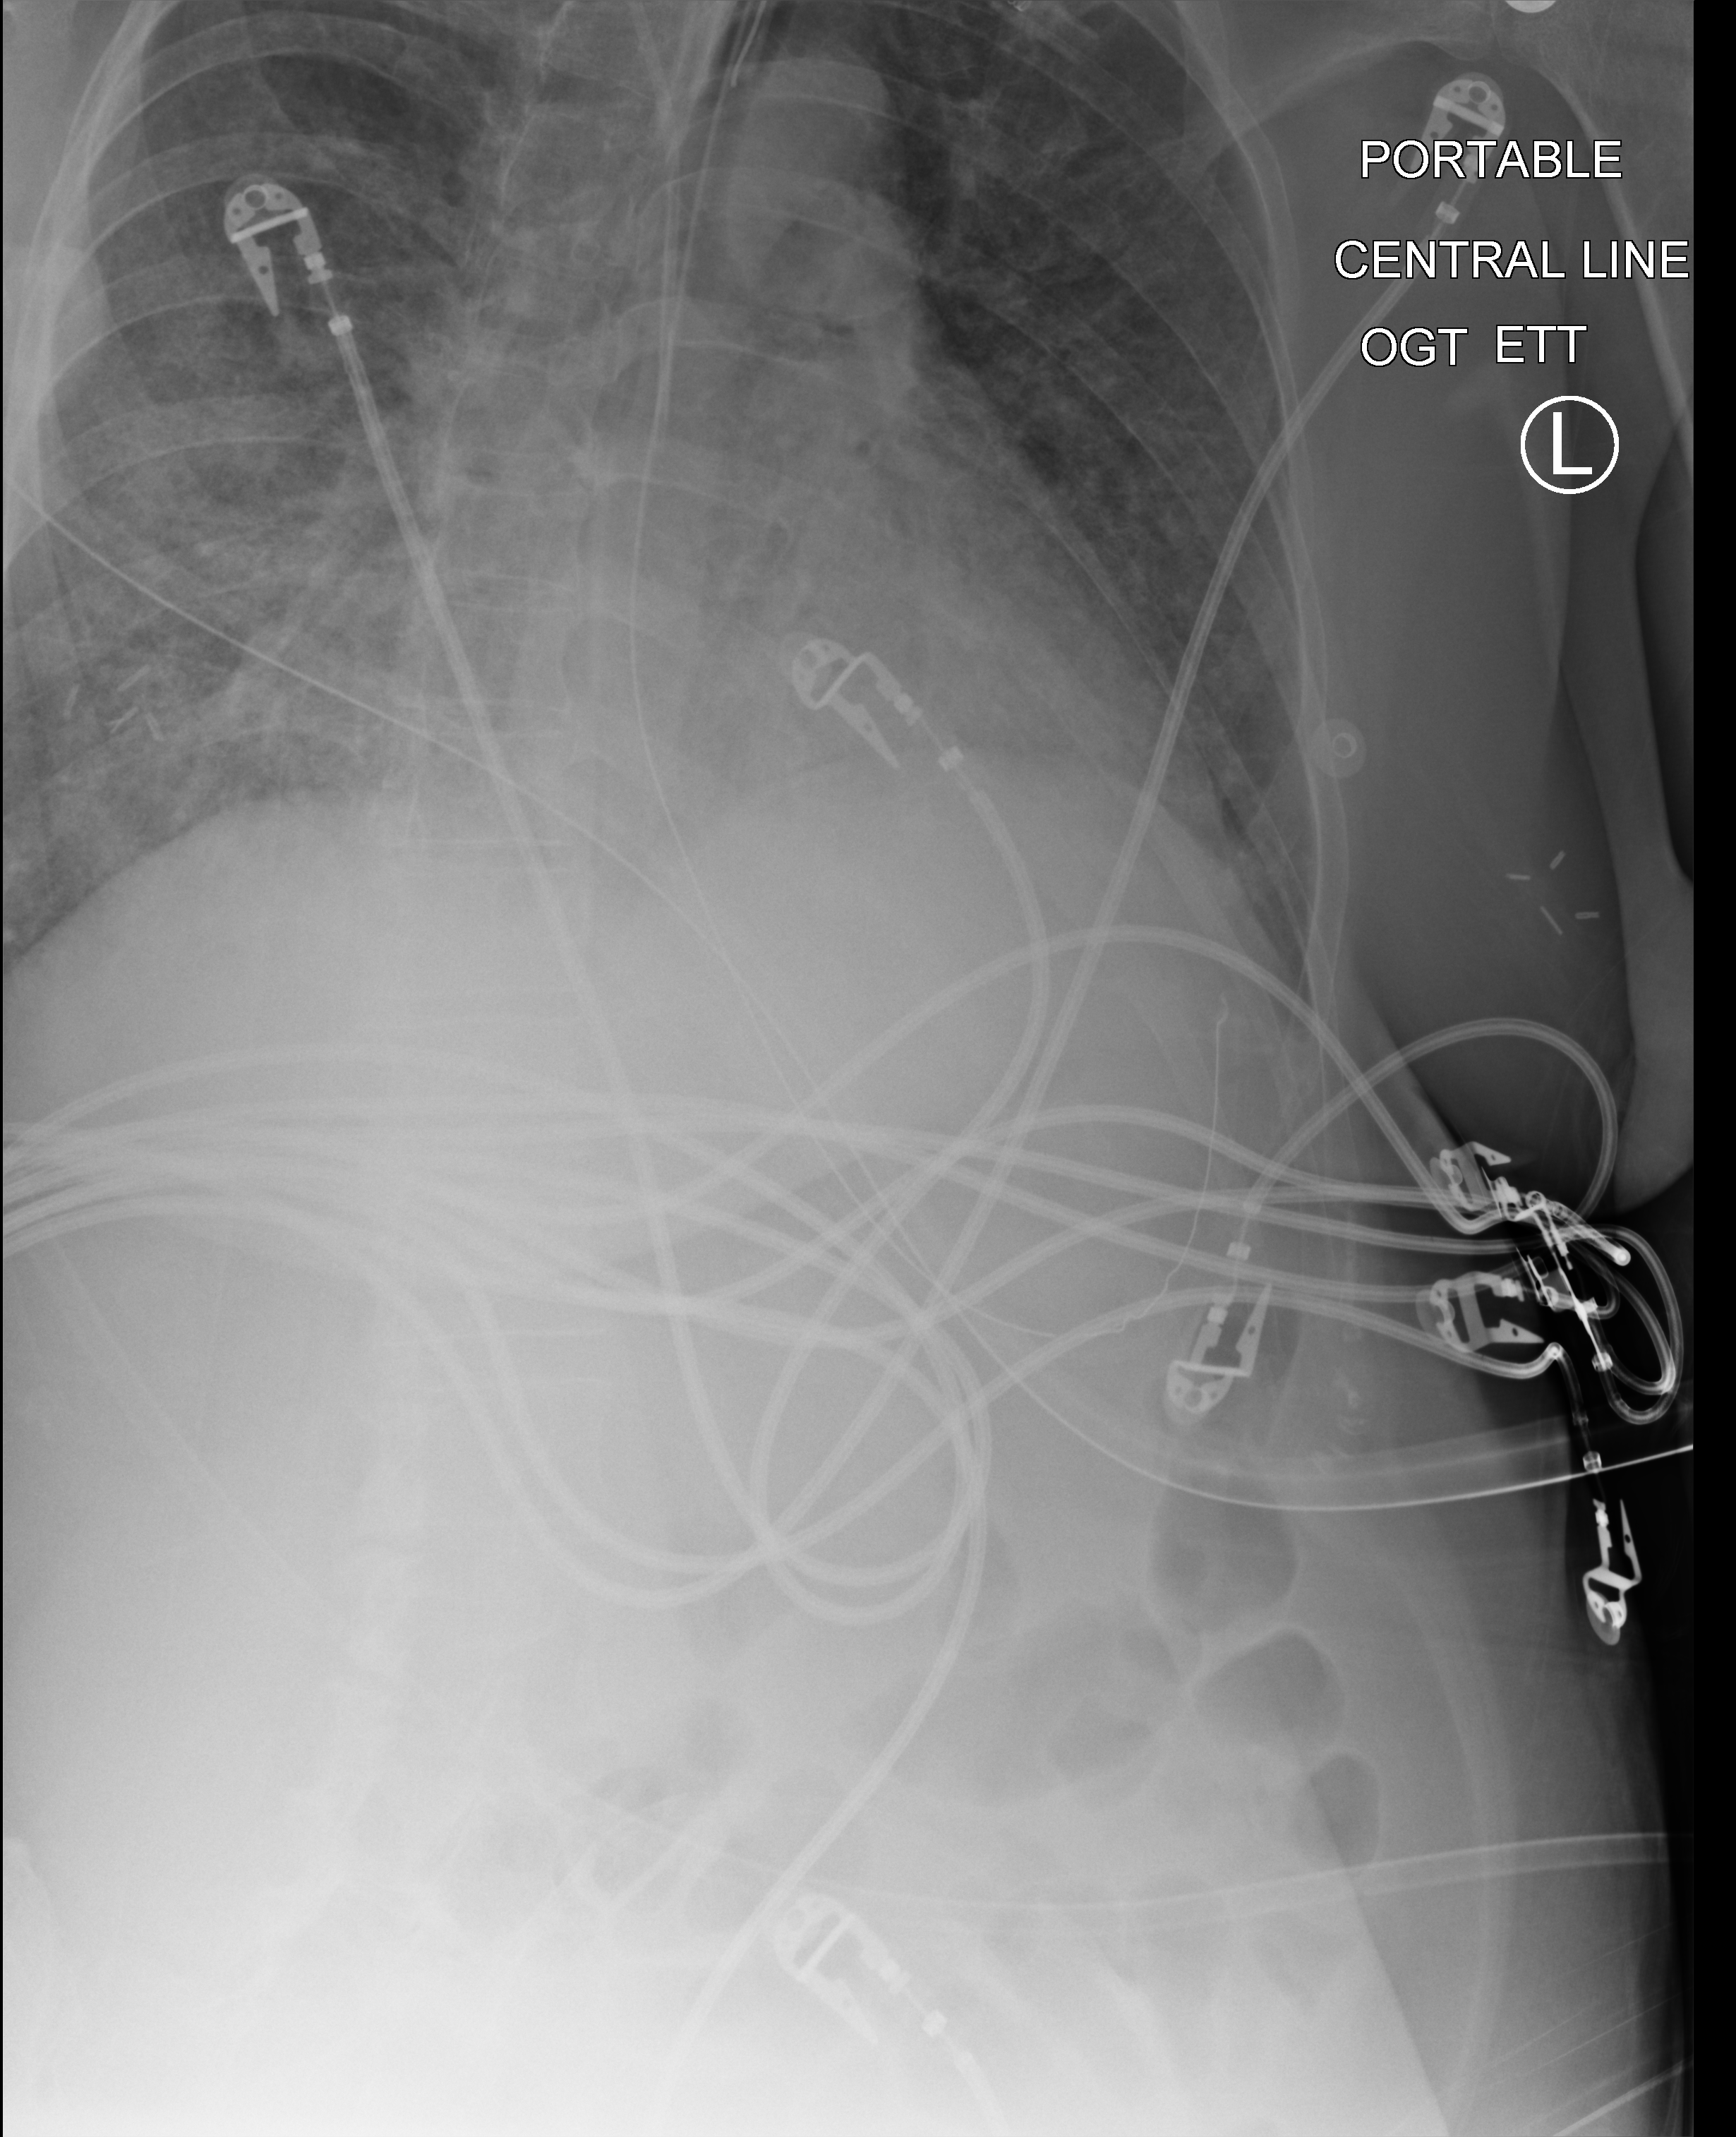
Chest X-ray (portable), anteroposterior (AP) projection. Patient hospitalised with COVID-19; female, aged 18–59 years.
From the hospital-stay record, not from the radiograph (when in the stay this image was taken is not recorded):
- admitted to intensive care during this hospital stay: no